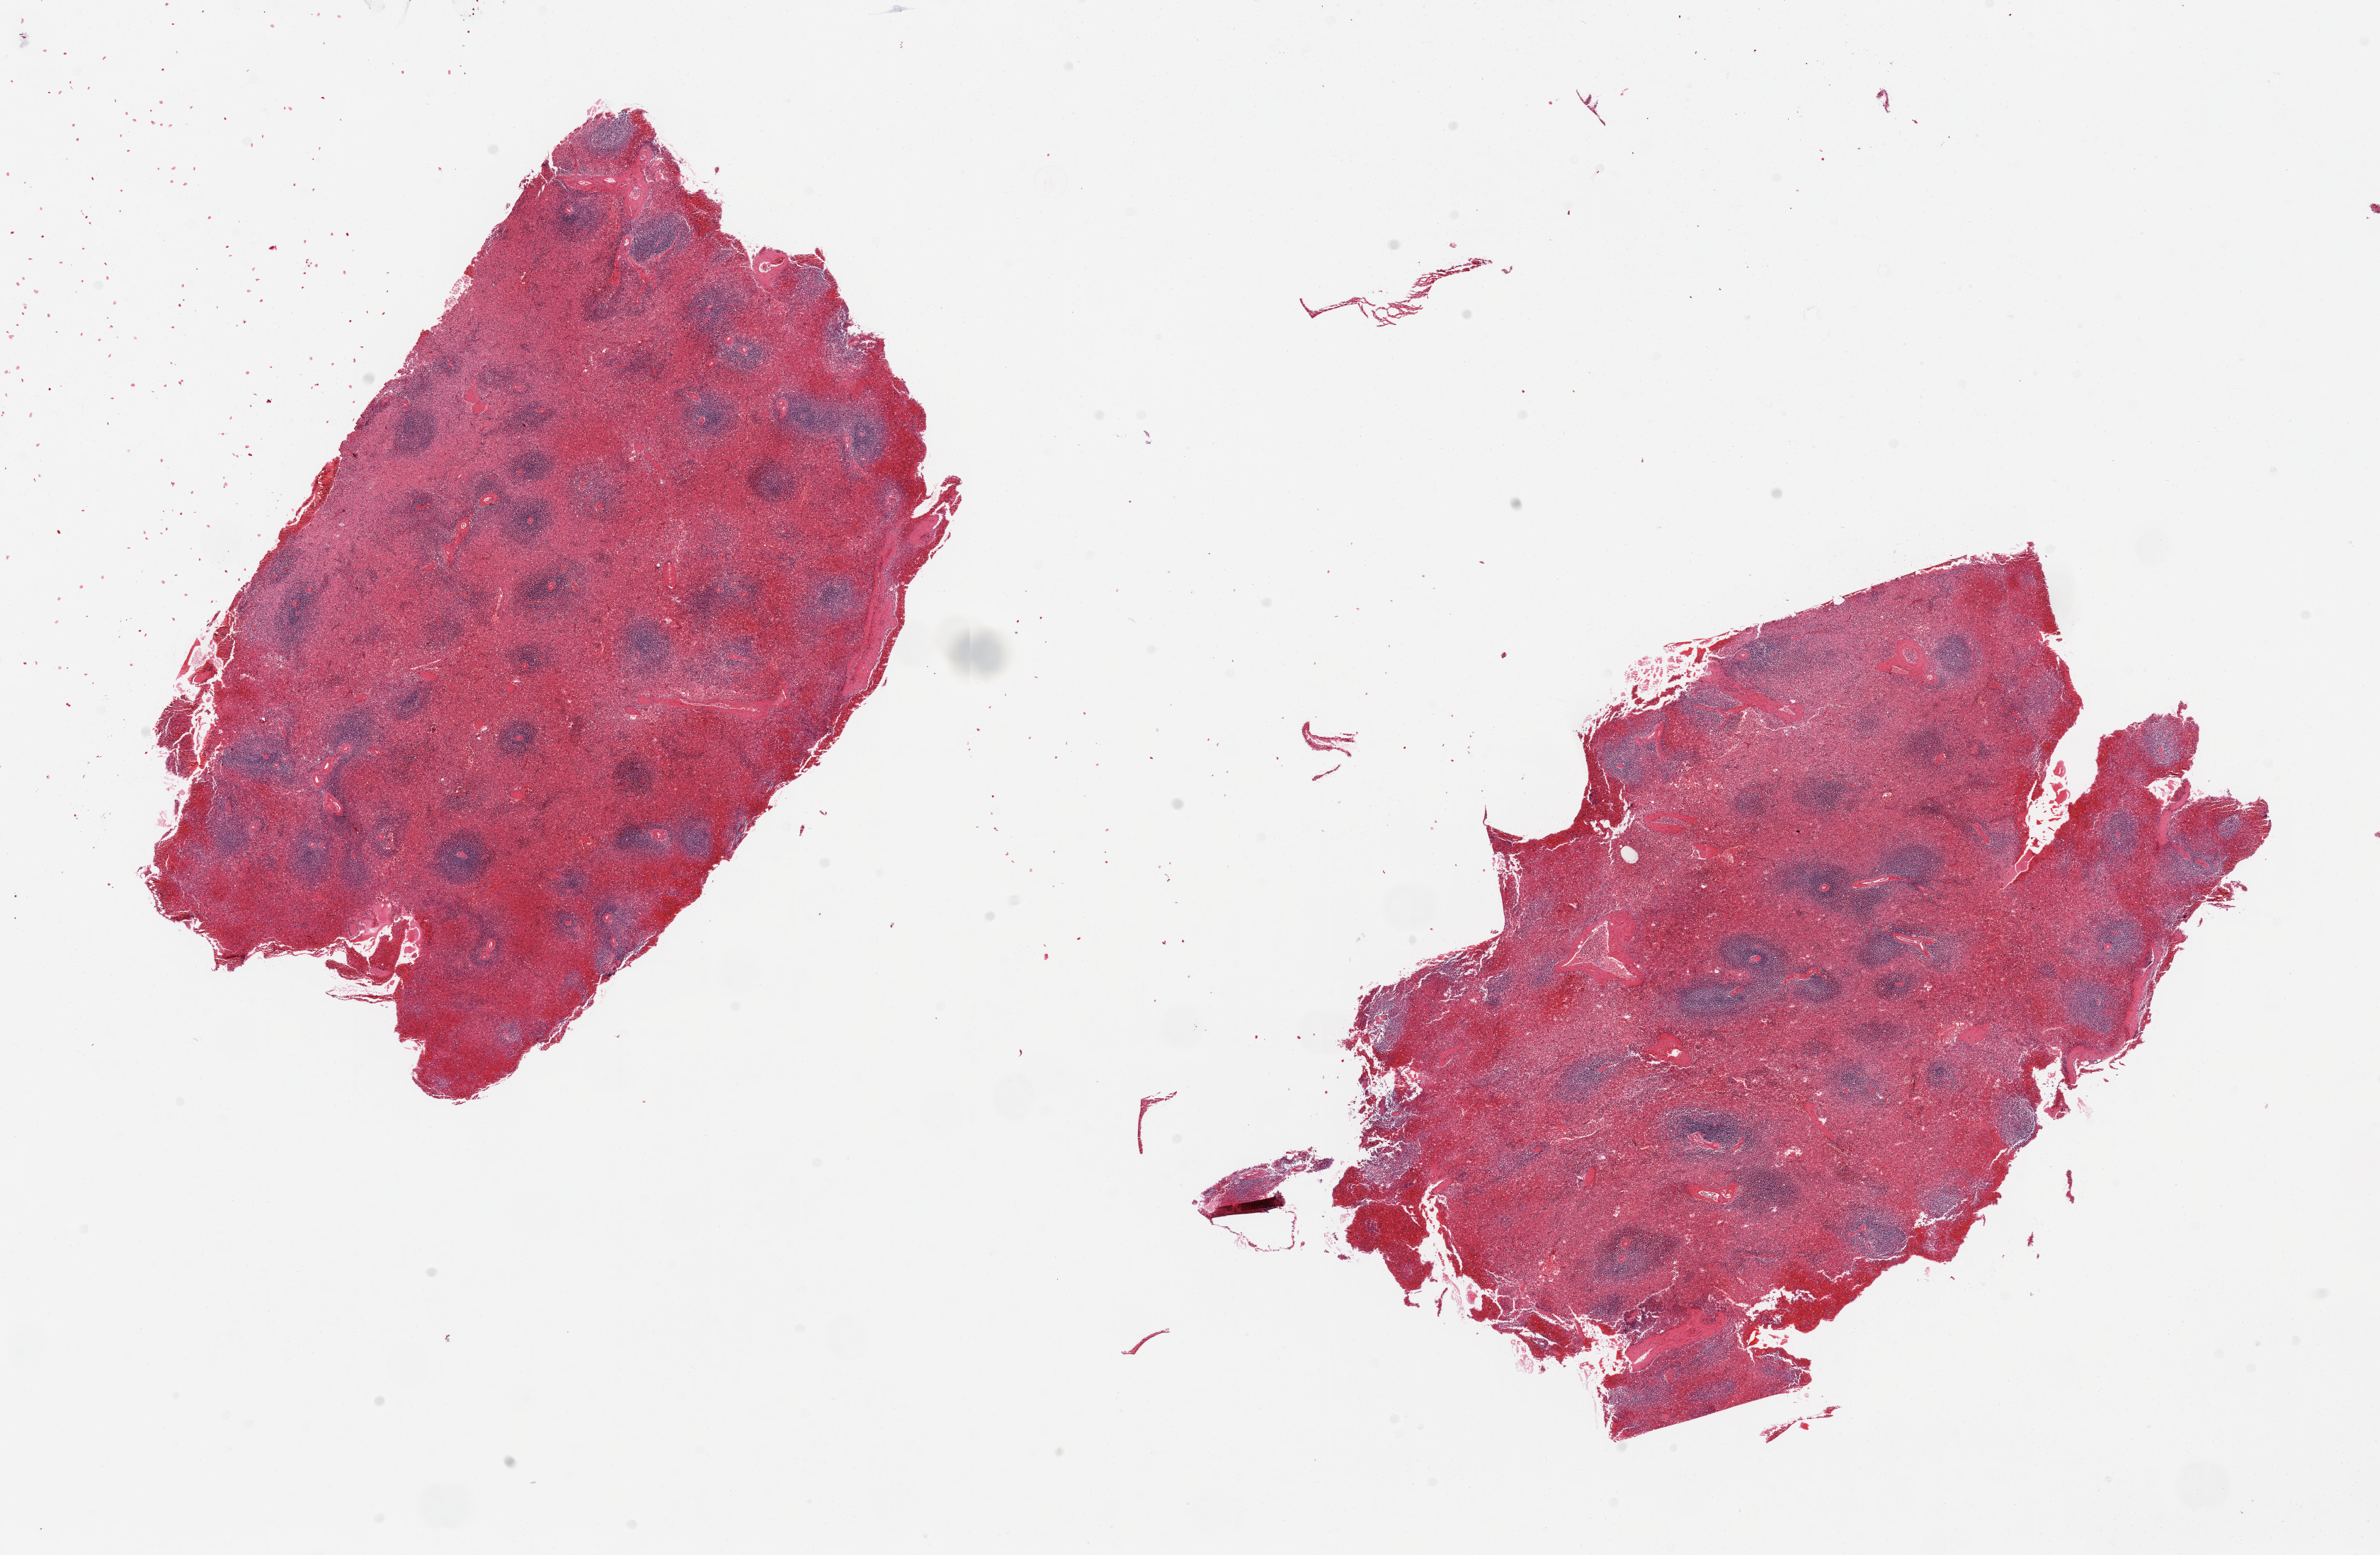
Whole-slide image, haematoxylin and eosin stain, brightfield, whole scanned area (about 26.6 x 17.4 mm, from a 20x scan) shown as a low-resolution overview, PAXgene-fixed, paraffin-embedded tissue, section of spleen (target tissue), donor tissue sample. Female donor.
- pathologist's review note for this sample: 2 pieces, congested